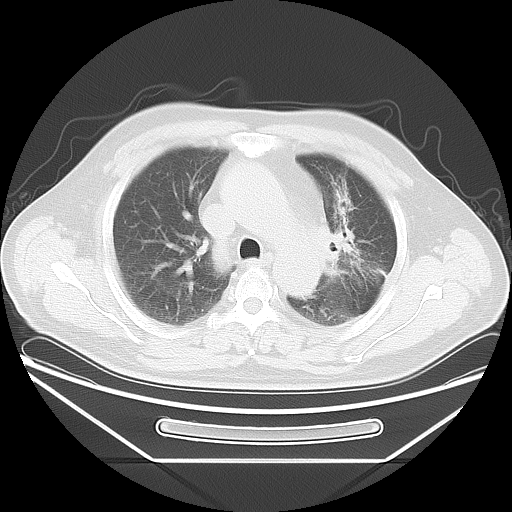
Chest CT, one axial slice; position 27 of 37 along the scan axis; 120 kVp; lung window (W 1500 / L -600 HU); 512 × 512 image matrix. Male patient, age 61 years. Case-level facts recorded for this patient, not image findings: clinical TNM (as recorded): T2a N0 M0.
Outlined on this slice (bounding box drawn by a radiologist):
- lung tumour (recorded histology: small cell carcinoma): bounding box [x1, y1, x2, y2] px = [310, 165, 389, 289]